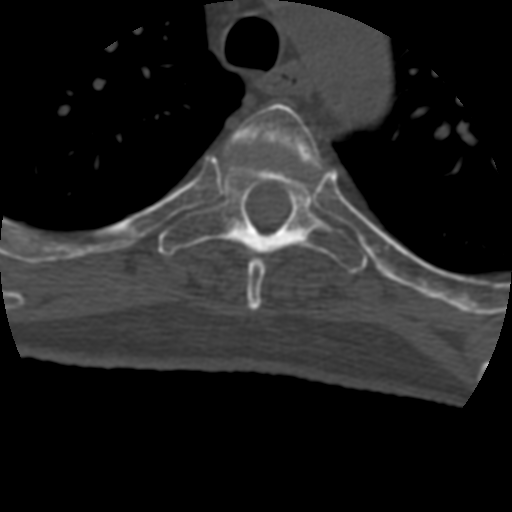
CT including the spine, one axial slice; slice 325 of 399 in the series (ordered by position); bone window (W 1800 / L 400 HU); 1.25 mm slice thickness; 512 × 512 image matrix, field of view 160 × 160 mm. Patient age 69 years. Case-level facts recorded for this patient, not image findings: primary cancer: prostate.
Structures marked on this image (semi-automatically segmented with operator editing):
- T4 vertebra: box from (x=233, y=103) to (x=321, y=311) px
- T5 vertebra: (x=158, y=152)–(x=368, y=274)